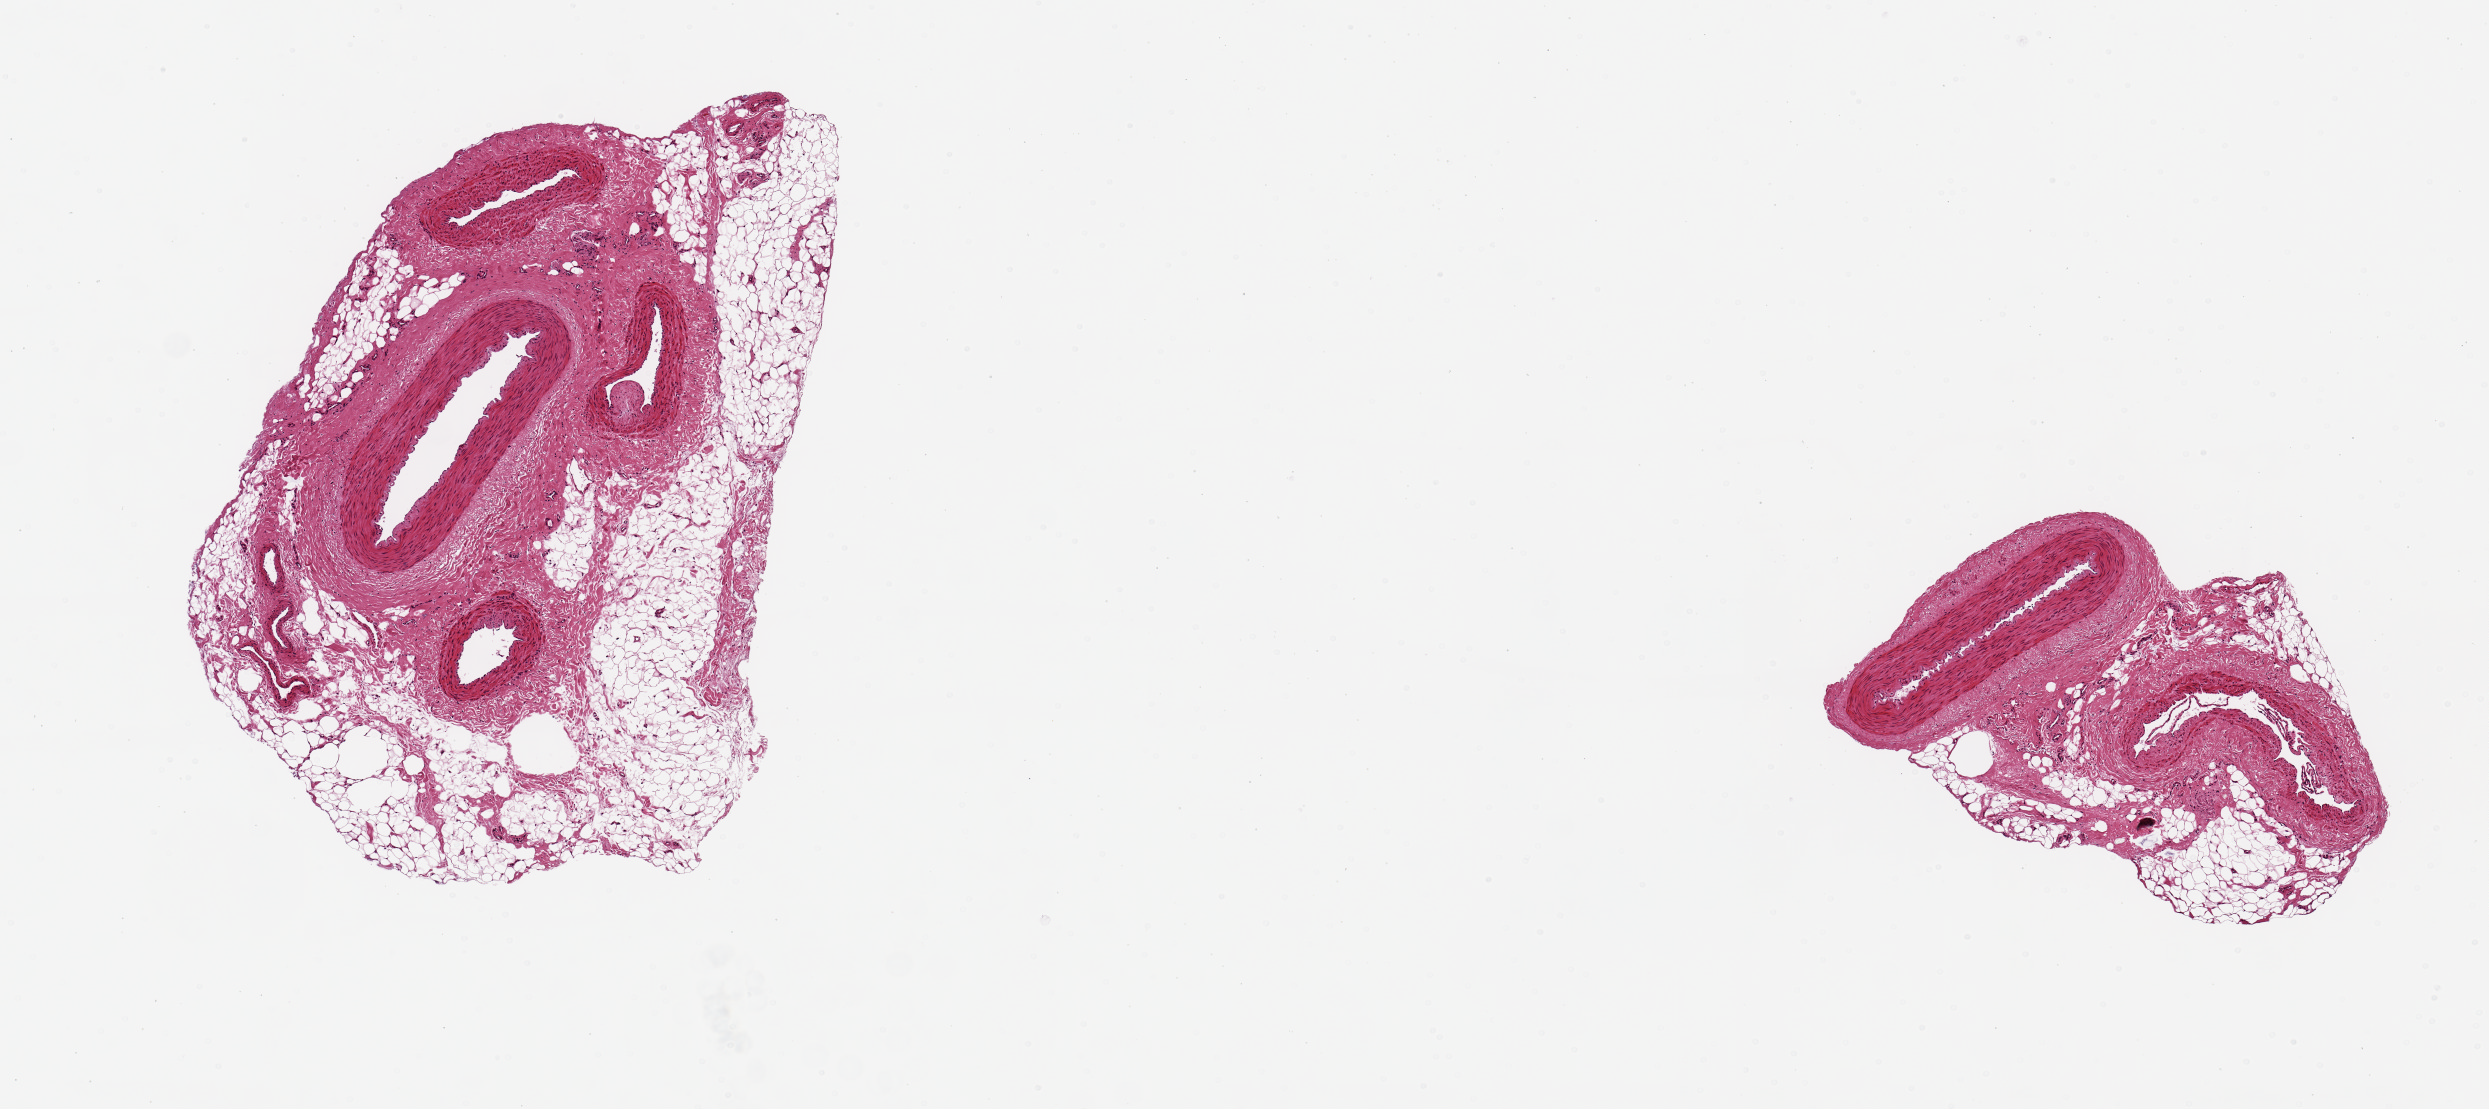
Whole-slide image, hematoxylin and eosin (H&E) stain, brightfield, whole scanned area (about 9.8 x 4.4 mm, slide scanned at 20x) shown as a low-resolution overview; PAXgene-fixed, paraffin-embedded tissue; sampled site (target tissue): tibial artery; tissue donor sample. Female donor.
* reviewer comment on this tissue sample: 2 pieces 1x2 & 3x2mm with 1x1.5 mm arteries and large amounts of adipose (~50% in the larger and ~40% in the other); large vein also in smaller piece